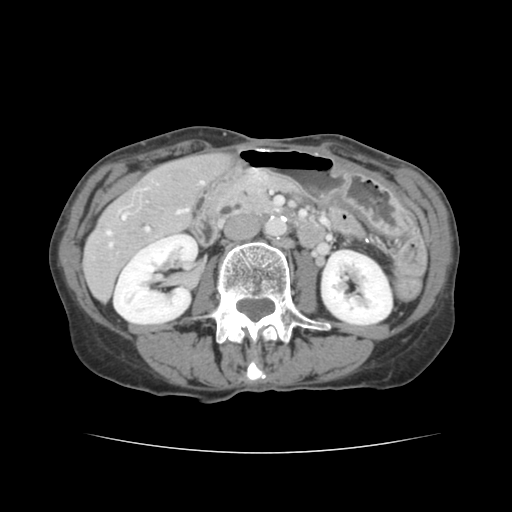
Contrast-enhanced abdominal CT, one axial slice. Slice 50 of 136 in the series (ordered by position). Intravenous contrast given. Soft-tissue window (W 400 / L 40 HU). 512 × 512 image matrix, field of view 319 × 319 mm. Female patient, age 77 years. Case-level facts recorded for this patient, not image findings: diagnosis: colorectal cancer liver metastases, imaged before liver resection; multiple liver metastases: yes; largest metastasis: 3 cm; disease in both lobes: no.
Structures marked on this image (manually delineated by an expert):
- hepatic veins: box from (x=107, y=181) to (x=203, y=247) px
- liver: (x=85, y=154)–(x=225, y=299)
- planned liver remnant (the part of the liver to remain after resection): (x=169, y=154)–(x=226, y=193)
- portal vein (with intrahepatic branches): (x=143, y=188)–(x=149, y=231)